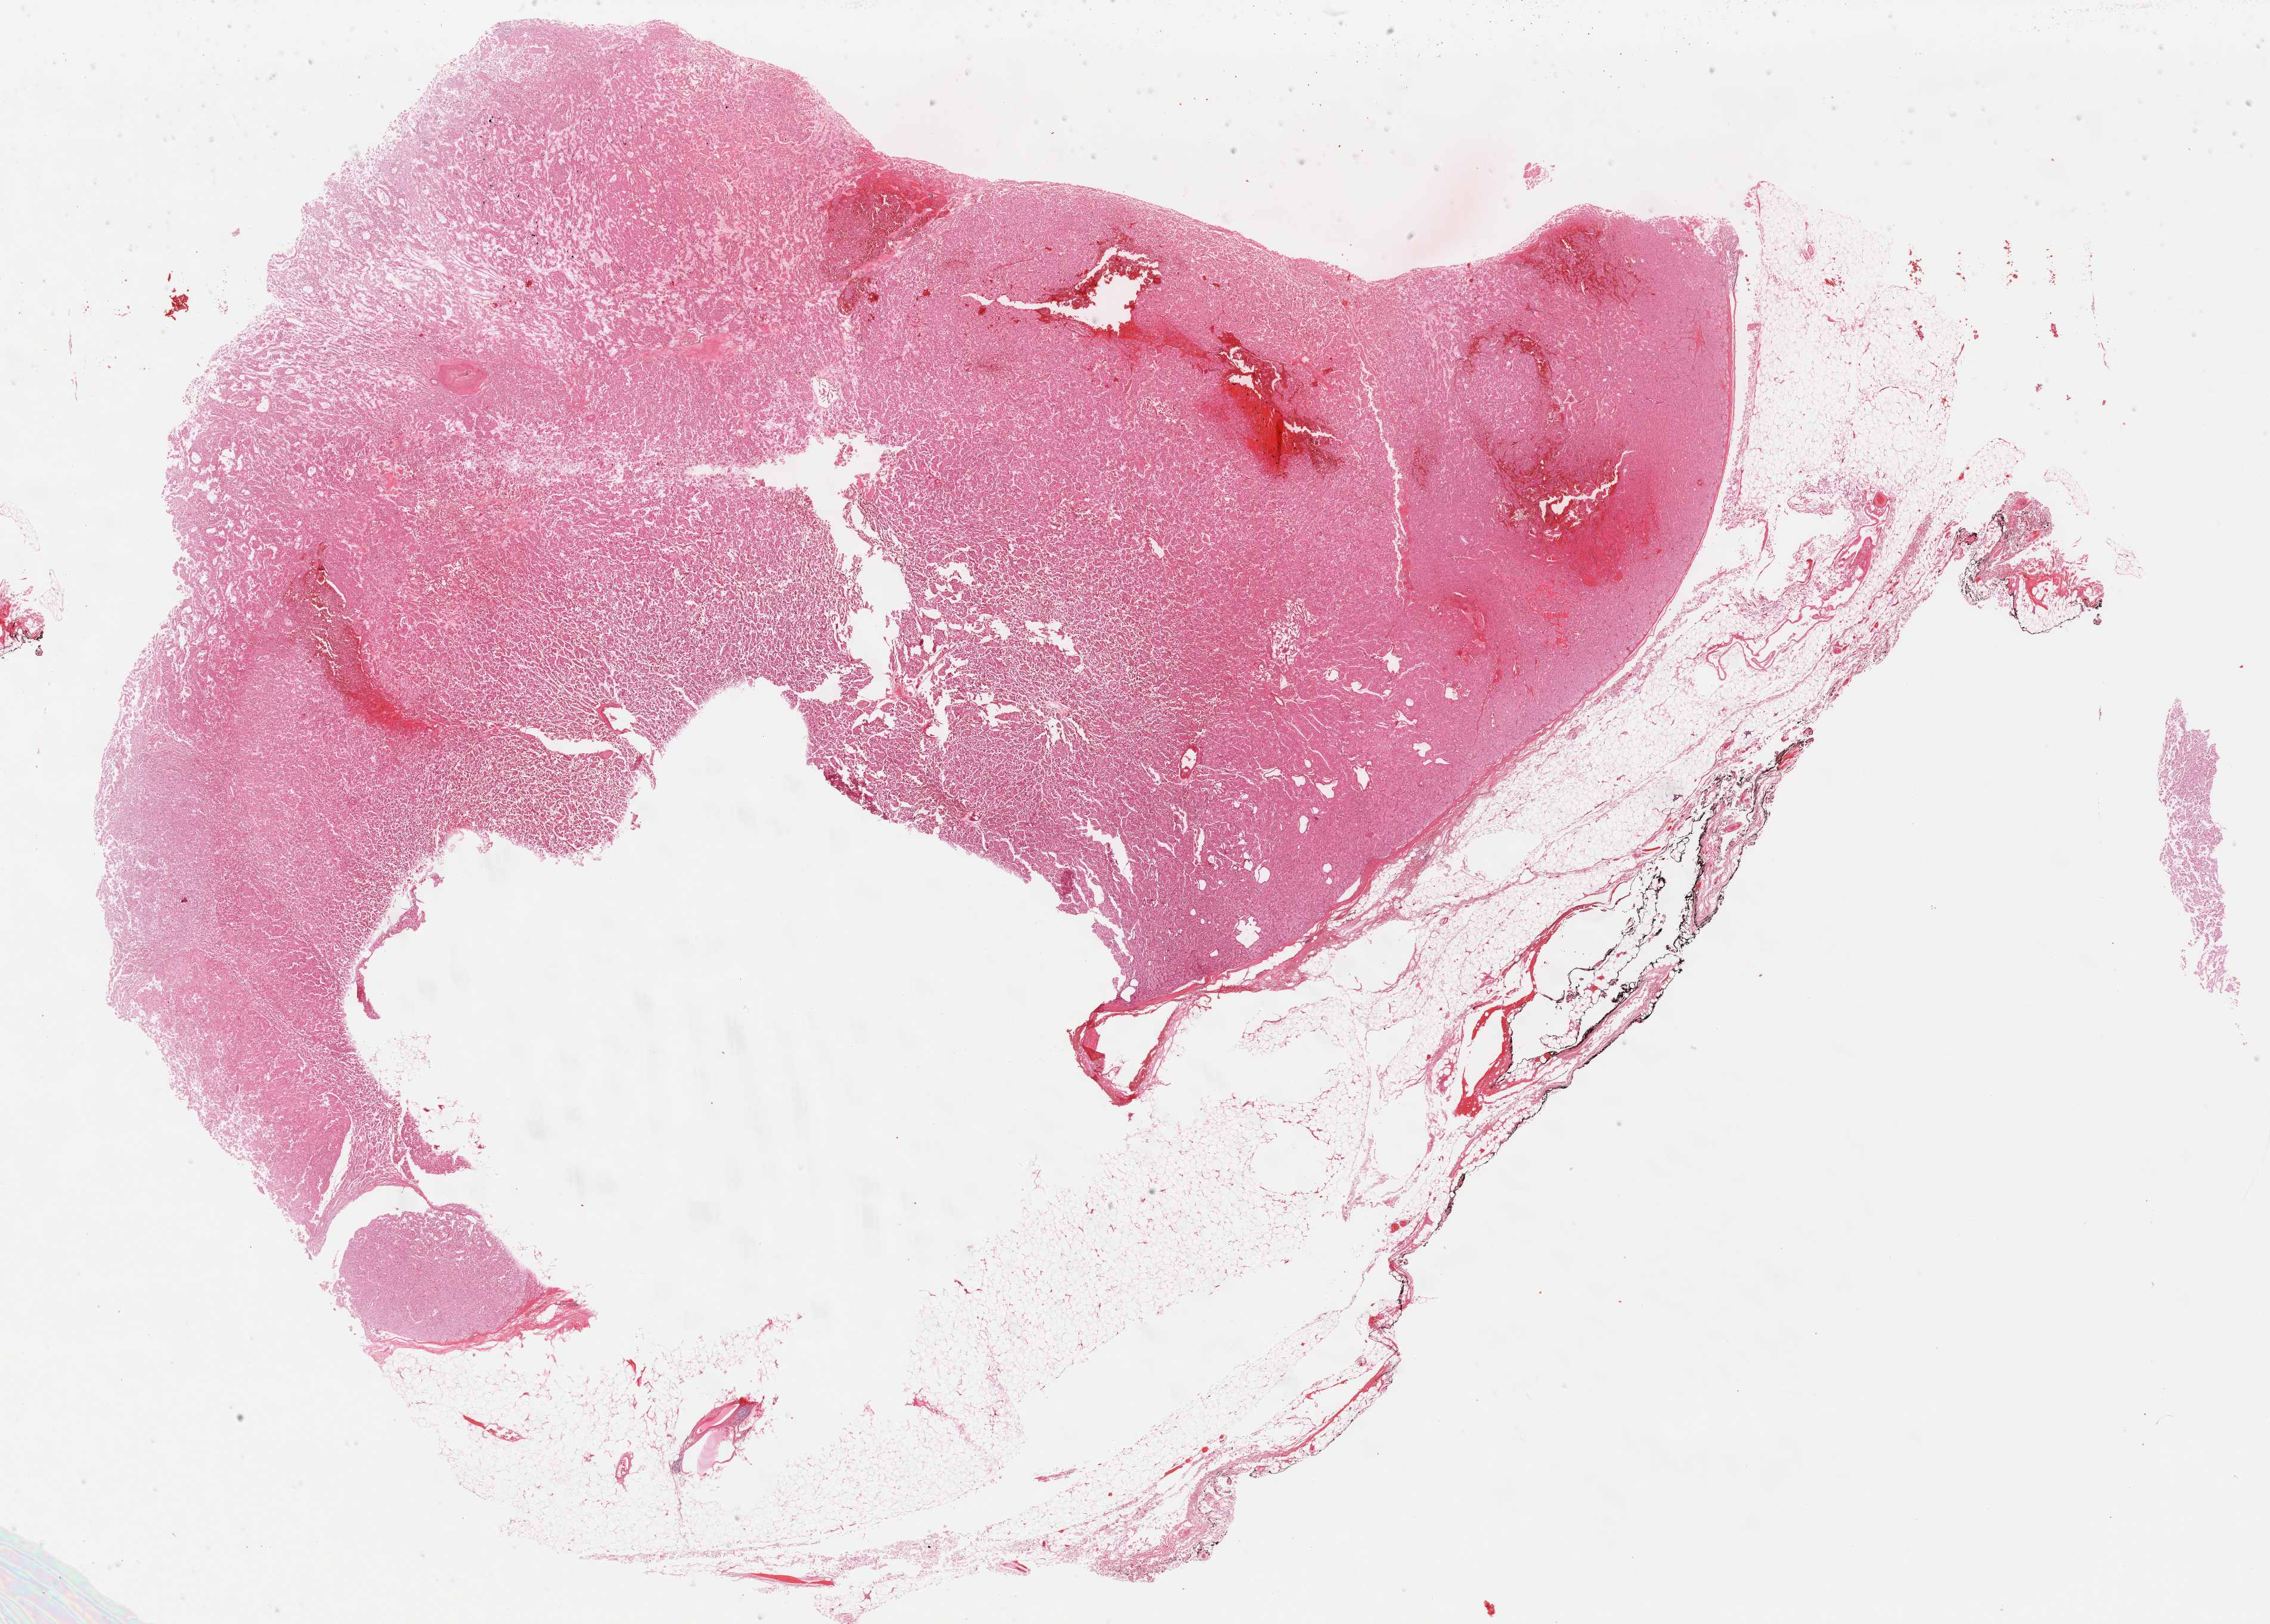
Whole-slide histology image, Hematoxylin and eosin (H&E) stained — shown as a low-resolution overview of the whole scanned area (about 30.7 x 22.0 mm, from a 40x scan). Formalin-fixed paraffin-embedded (FFPE) diagnostic section. Sample: primary tumour, kidney. Patient: male, age at initial diagnosis 44 years.
Diagnosis: Renal cell carcinoma, chromophobe type. Lymph nodes positive (case pathology): 0 of 6 examined. AJCC pathologic stage: I (6th edition).